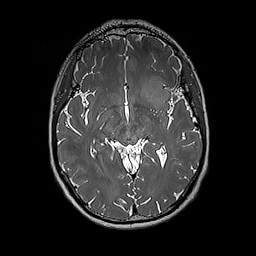
Brain MRI from a brain-tumour surgery series, one axial slice. Position 106 of 192 along the scan axis. 1 mm slice thickness. 256 × 256 image matrix, field of view 250 × 250 mm. Case-level facts recorded for this patient, not image findings: histopathology: Glioblastoma; WHO grade: 4; IDH mutation: no; tumour location: Left Insular.
Annotated regions visible in this slice (manually delineated by an expert):
- tumour: bounding box (x1, y1, x2, y2) in pixels: (140, 76, 171, 109)